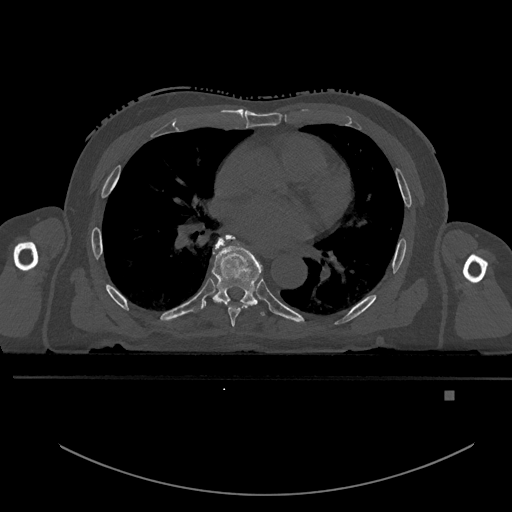
CT including the spine, one axial slice. Slice 277 of 969 in the series (ordered by position). Bone window (W 1800 / L 400 HU). 0.5 mm slice thickness. 512 × 512 image matrix, field of view 456 × 456 mm. Male patient, age 82 years. Case-level facts recorded for this patient, not image findings: primary cancer: prostate.
Annotated regions visible in this slice (semi-automatic segmentation, software-assisted and operator-edited):
- T6 vertebra: bounding box [x1, y1, x2, y2] px = [215, 237, 250, 327]
- T7 vertebra: [204, 235, 265, 316]